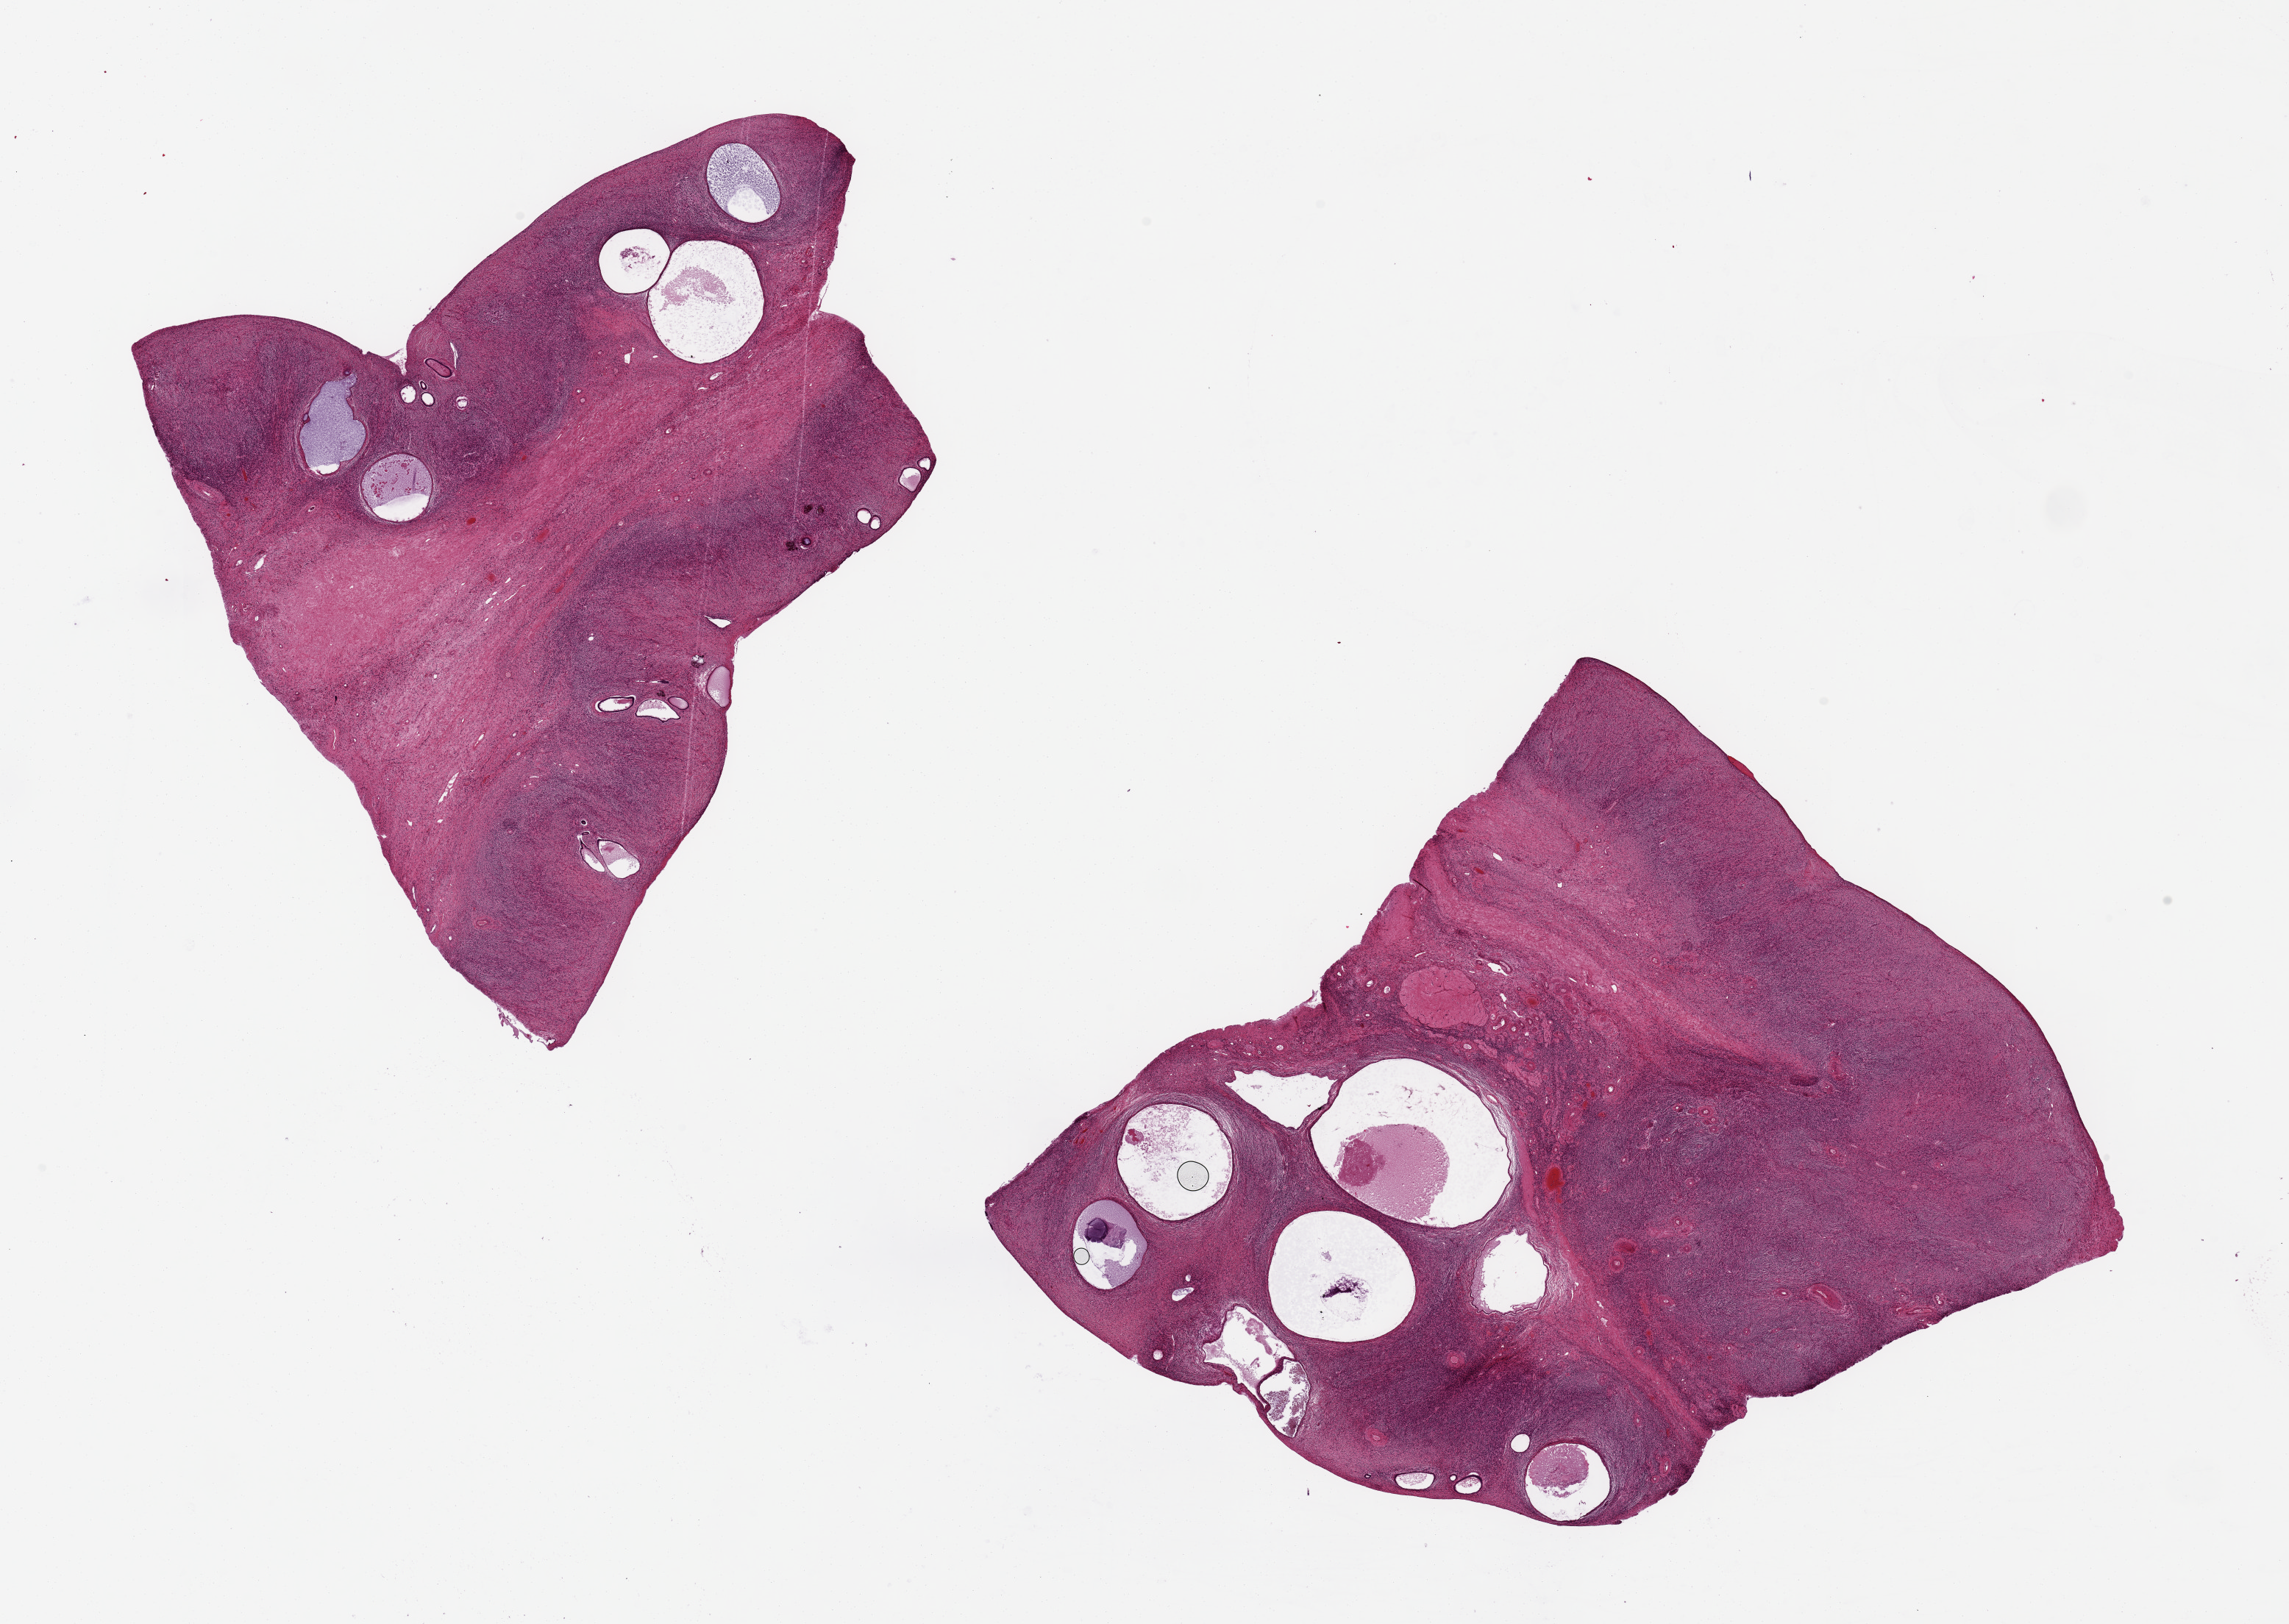
Hematoxylin and eosin (H&E) whole-slide image — low-resolution overview of the scanned area, about 24.6 x 17.5 mm; PAXgene-fixed paraffin-embedded (PFPE) section; target tissue: ovary; donor tissue sample. Donor sex: female.
Review note (as recorded): 2 pieces 9x8 & 8x8 mm; atrophic, partly cystic.